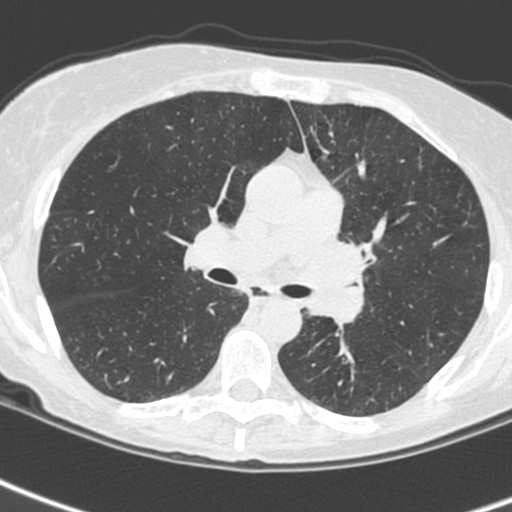
Low-dose screening chest CT, one axial slice; slice 148 of 242 in the series (ordered by position); lung window (W 1500 / L -600 HU); 512 × 512 image matrix, field of view 284 × 284 mm.
Outlined on this slice (manually delineated by an expert):
- lesion 3 (tumor, upper lobe of left lung): bounding box <307,241,365,326> (left, top, right, bottom; pixels)